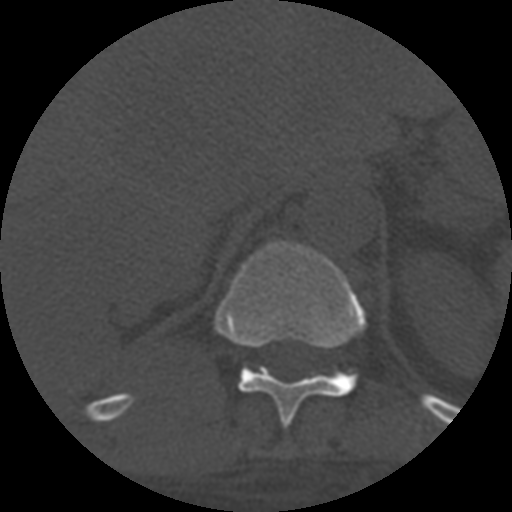
CT including the spine, one axial slice. Position 332 of 708 along the scan axis. Reconstruction kernel STANDARD. 120 kVp. One of 3 acquisitions stored at this slice position. Bone window (W 1800 / L 400 HU). 1.25 mm slice thickness. 512 × 512 image matrix, field of view 160 × 160 mm. Patient age 55 years. From the clinical record (not read from this slice): primary cancer: colon.
Annotated regions visible in this slice (semi-automatic segmentation, software-assisted and operator-edited):
- T11 vertebra: bounding box (x1, y1, x2, y2) in pixels: (216, 240, 367, 428)